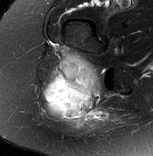
MRI of an extremity soft-tissue mass, one axial slice; position 51 of 77 along the scan axis; T2-weighted fat-saturated; MR volume resampled by the dataset authors to the PET/CT grid (not the native acquisition matrix); 3.27 mm slice thickness; 153 × 156 image matrix. Female patient. Case-level facts recorded for this patient, not image findings: histological type: synovial sarcoma; grade: intermediate; site of the primary tumour: right buttock.
Outlined on this slice (expert contour drawn on MRI and transferred to this co-registered scan by the dataset authors):
- gross tumour volume including surrounding oedema: bounding box <46,56,109,128> (left, top, right, bottom; pixels)
- gross tumour volume (mass): <46,56,100,110>